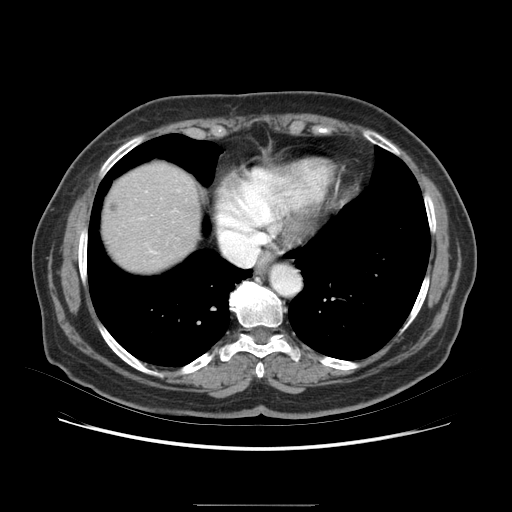
Contrast-enhanced abdominal CT (liver protocol), one axial slice. Position 73 of 79 along the scan axis. Soft-tissue window (W 400 / L 40 HU). 2.5 mm slice thickness. 512 × 512 image matrix. Case-level facts recorded for this patient, not image findings: diagnosis: hepatocellular carcinoma (patient treated with transarterial chemoembolisation; whether this scan precedes or follows treatment is not stated here); TNM stage (as recorded): Stage-I; Child-Pugh class: A; tumour differentiation: poorly differentiated; tumour nodularity: uninodular.
Annotated regions visible in this slice (semi-automatic segmentation, software-assisted and operator-edited):
- liver parenchyma outside the tumour (the mass and vessels are separate outlines, so this box may not span the whole liver): bounding box <124,176,186,240> (left, top, right, bottom; pixels)